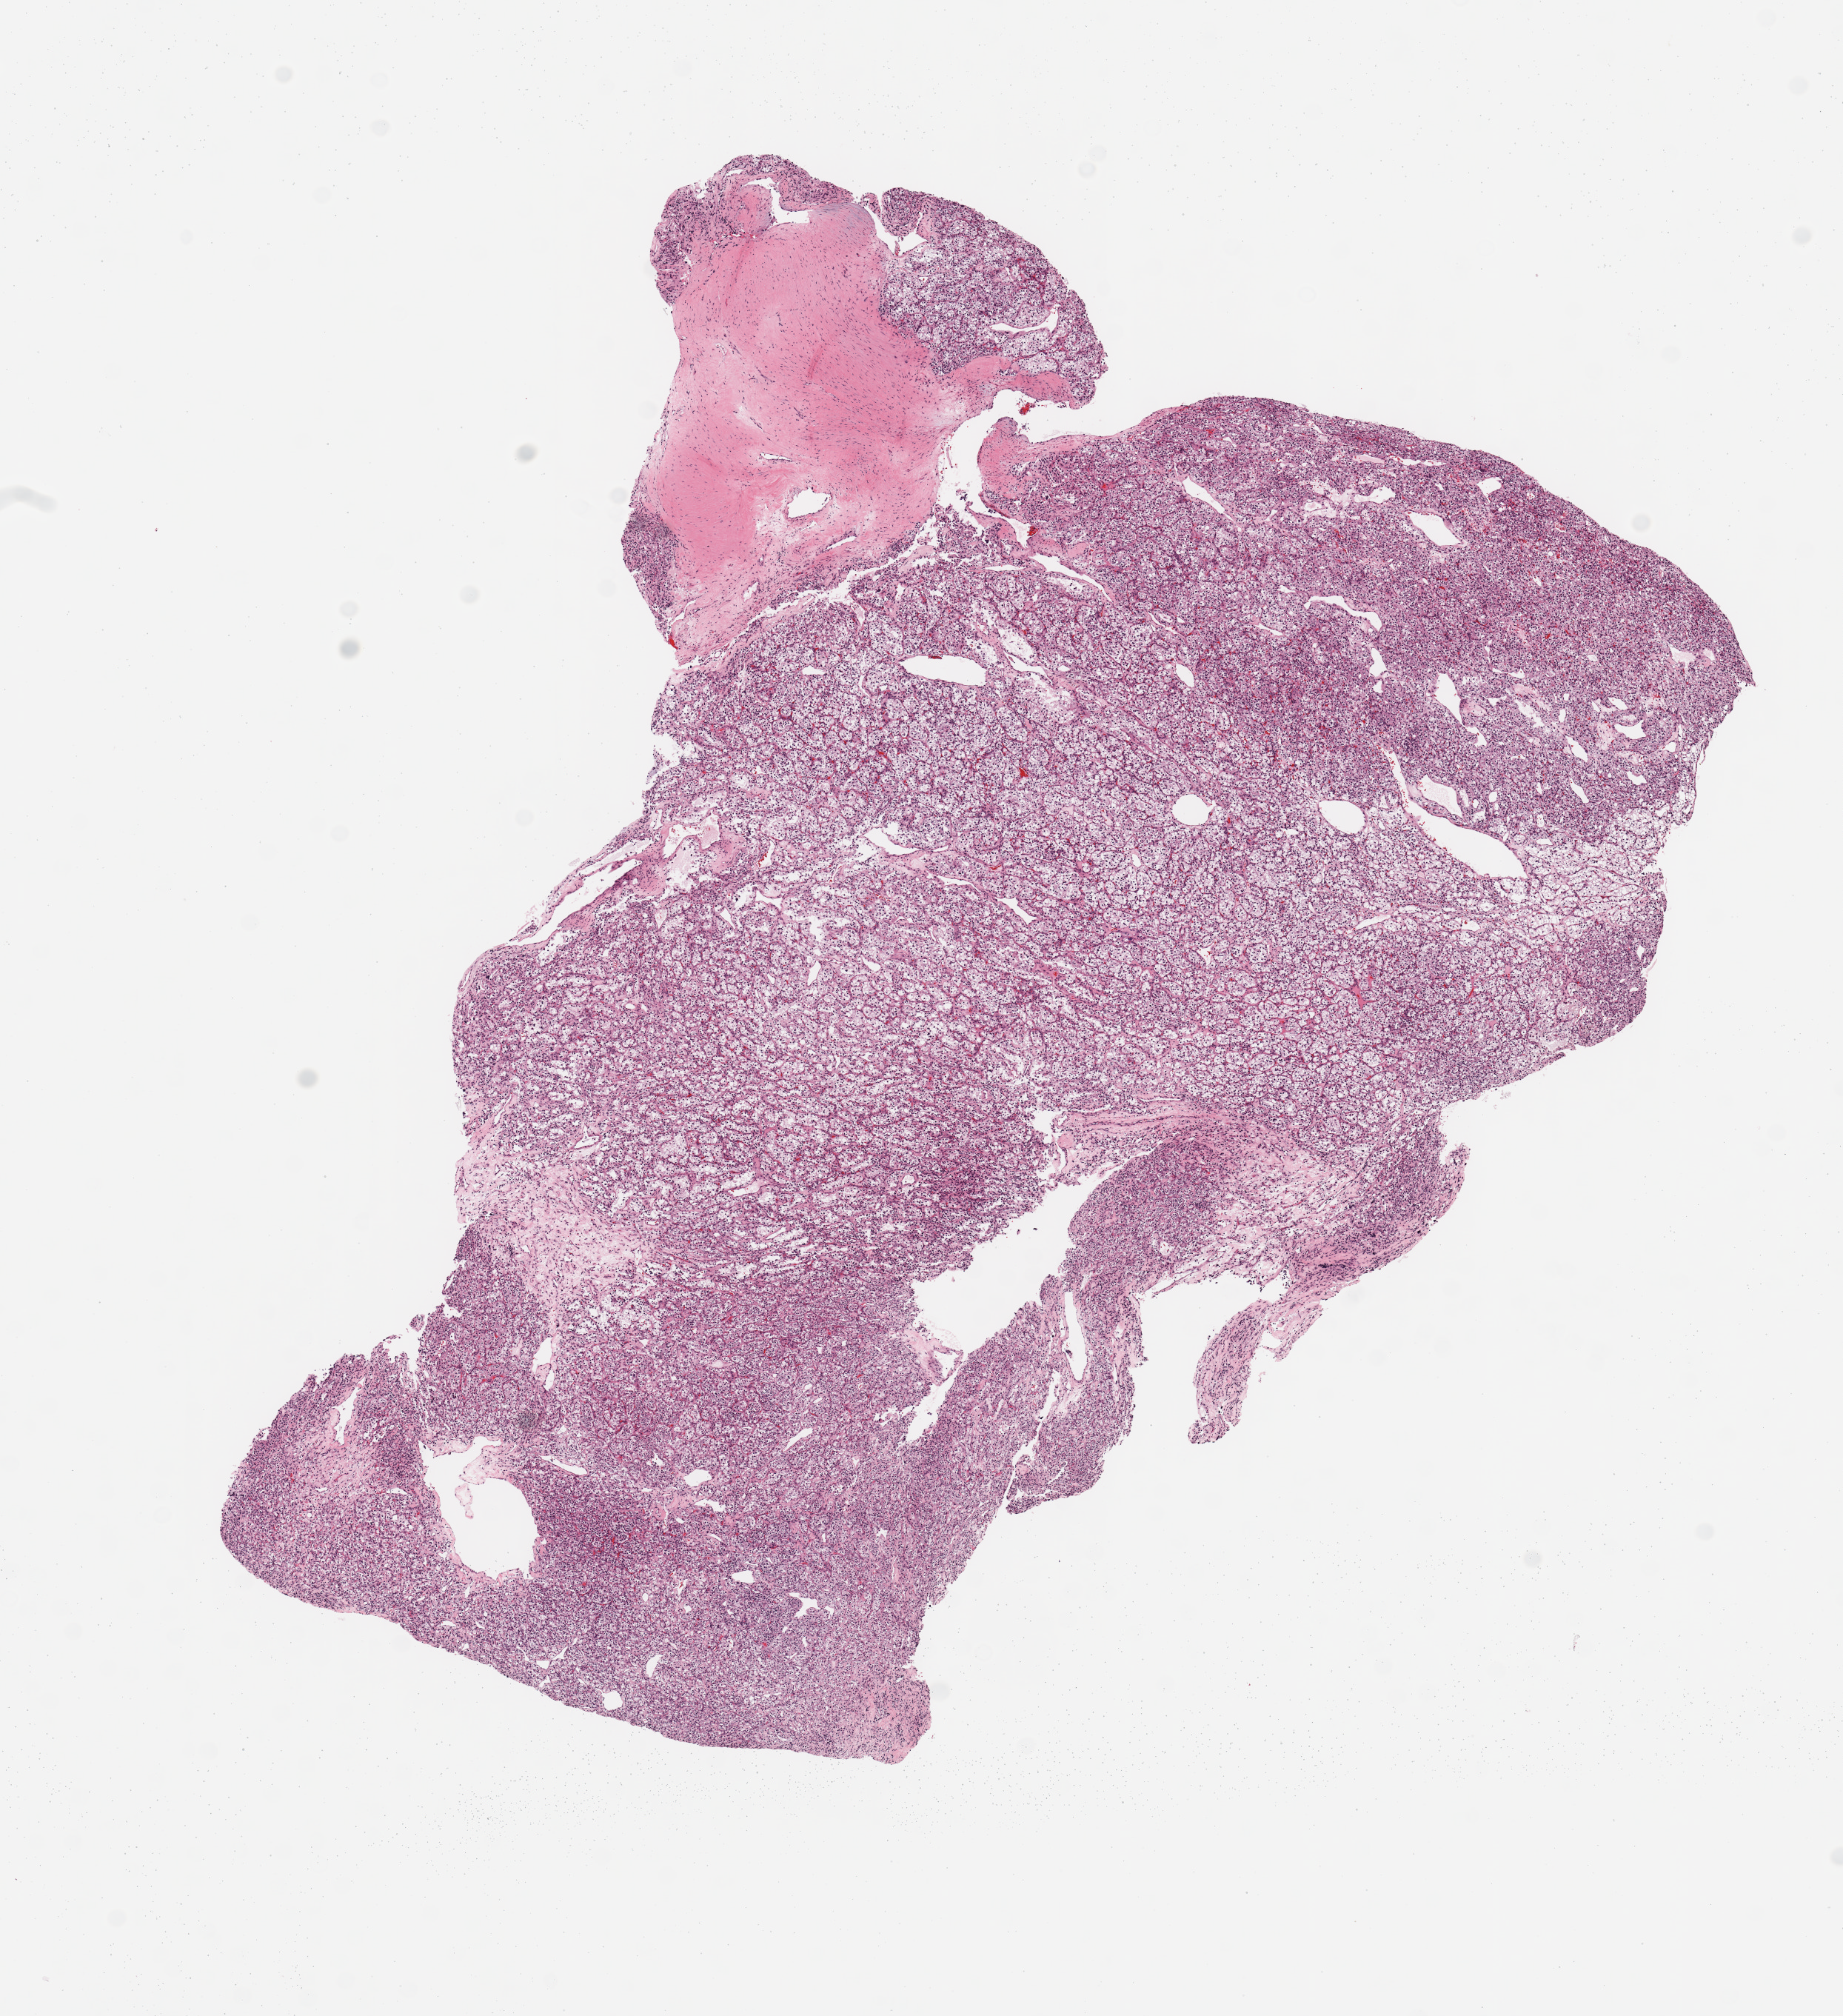
H&E-stained whole-slide image, a low-resolution overview of the entire scanned area, about 9.8 x 10.8 mm, kidney, tumour tissue. Male, 66 y/o. Histologic grade: G4 (undifferentiated).
• AJCC pathologic stage: IV
• histologic diagnosis: Renal cell carcinoma, NOS
• primary tumour site (as recorded): lower pole